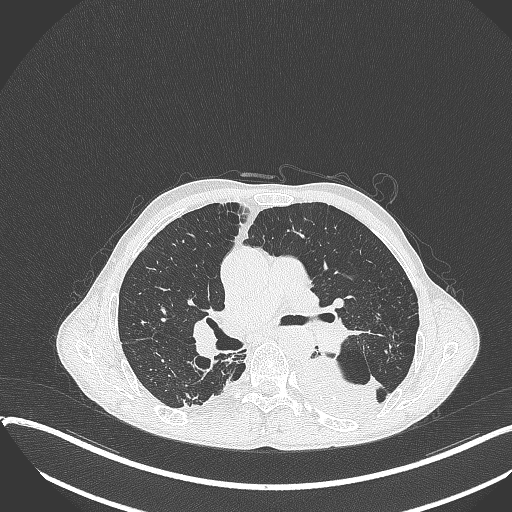
Chest CT, one axial slice. Reconstruction kernel B70f. 120 kVp. Lung window (W 1500 / L -600 HU). 1 mm slice thickness. 512 × 512 image matrix, field of view 400 × 400 mm. Male patient, age 57 years. Case-level facts recorded for this patient, not image findings: clinical TNM (as recorded): T4 N0 M0.
Outlined on this slice (rectangle marked by the reading radiologist):
- lung tumour (recorded histology: squamous cell carcinoma): box from (x=295, y=353) to (x=383, y=421) px